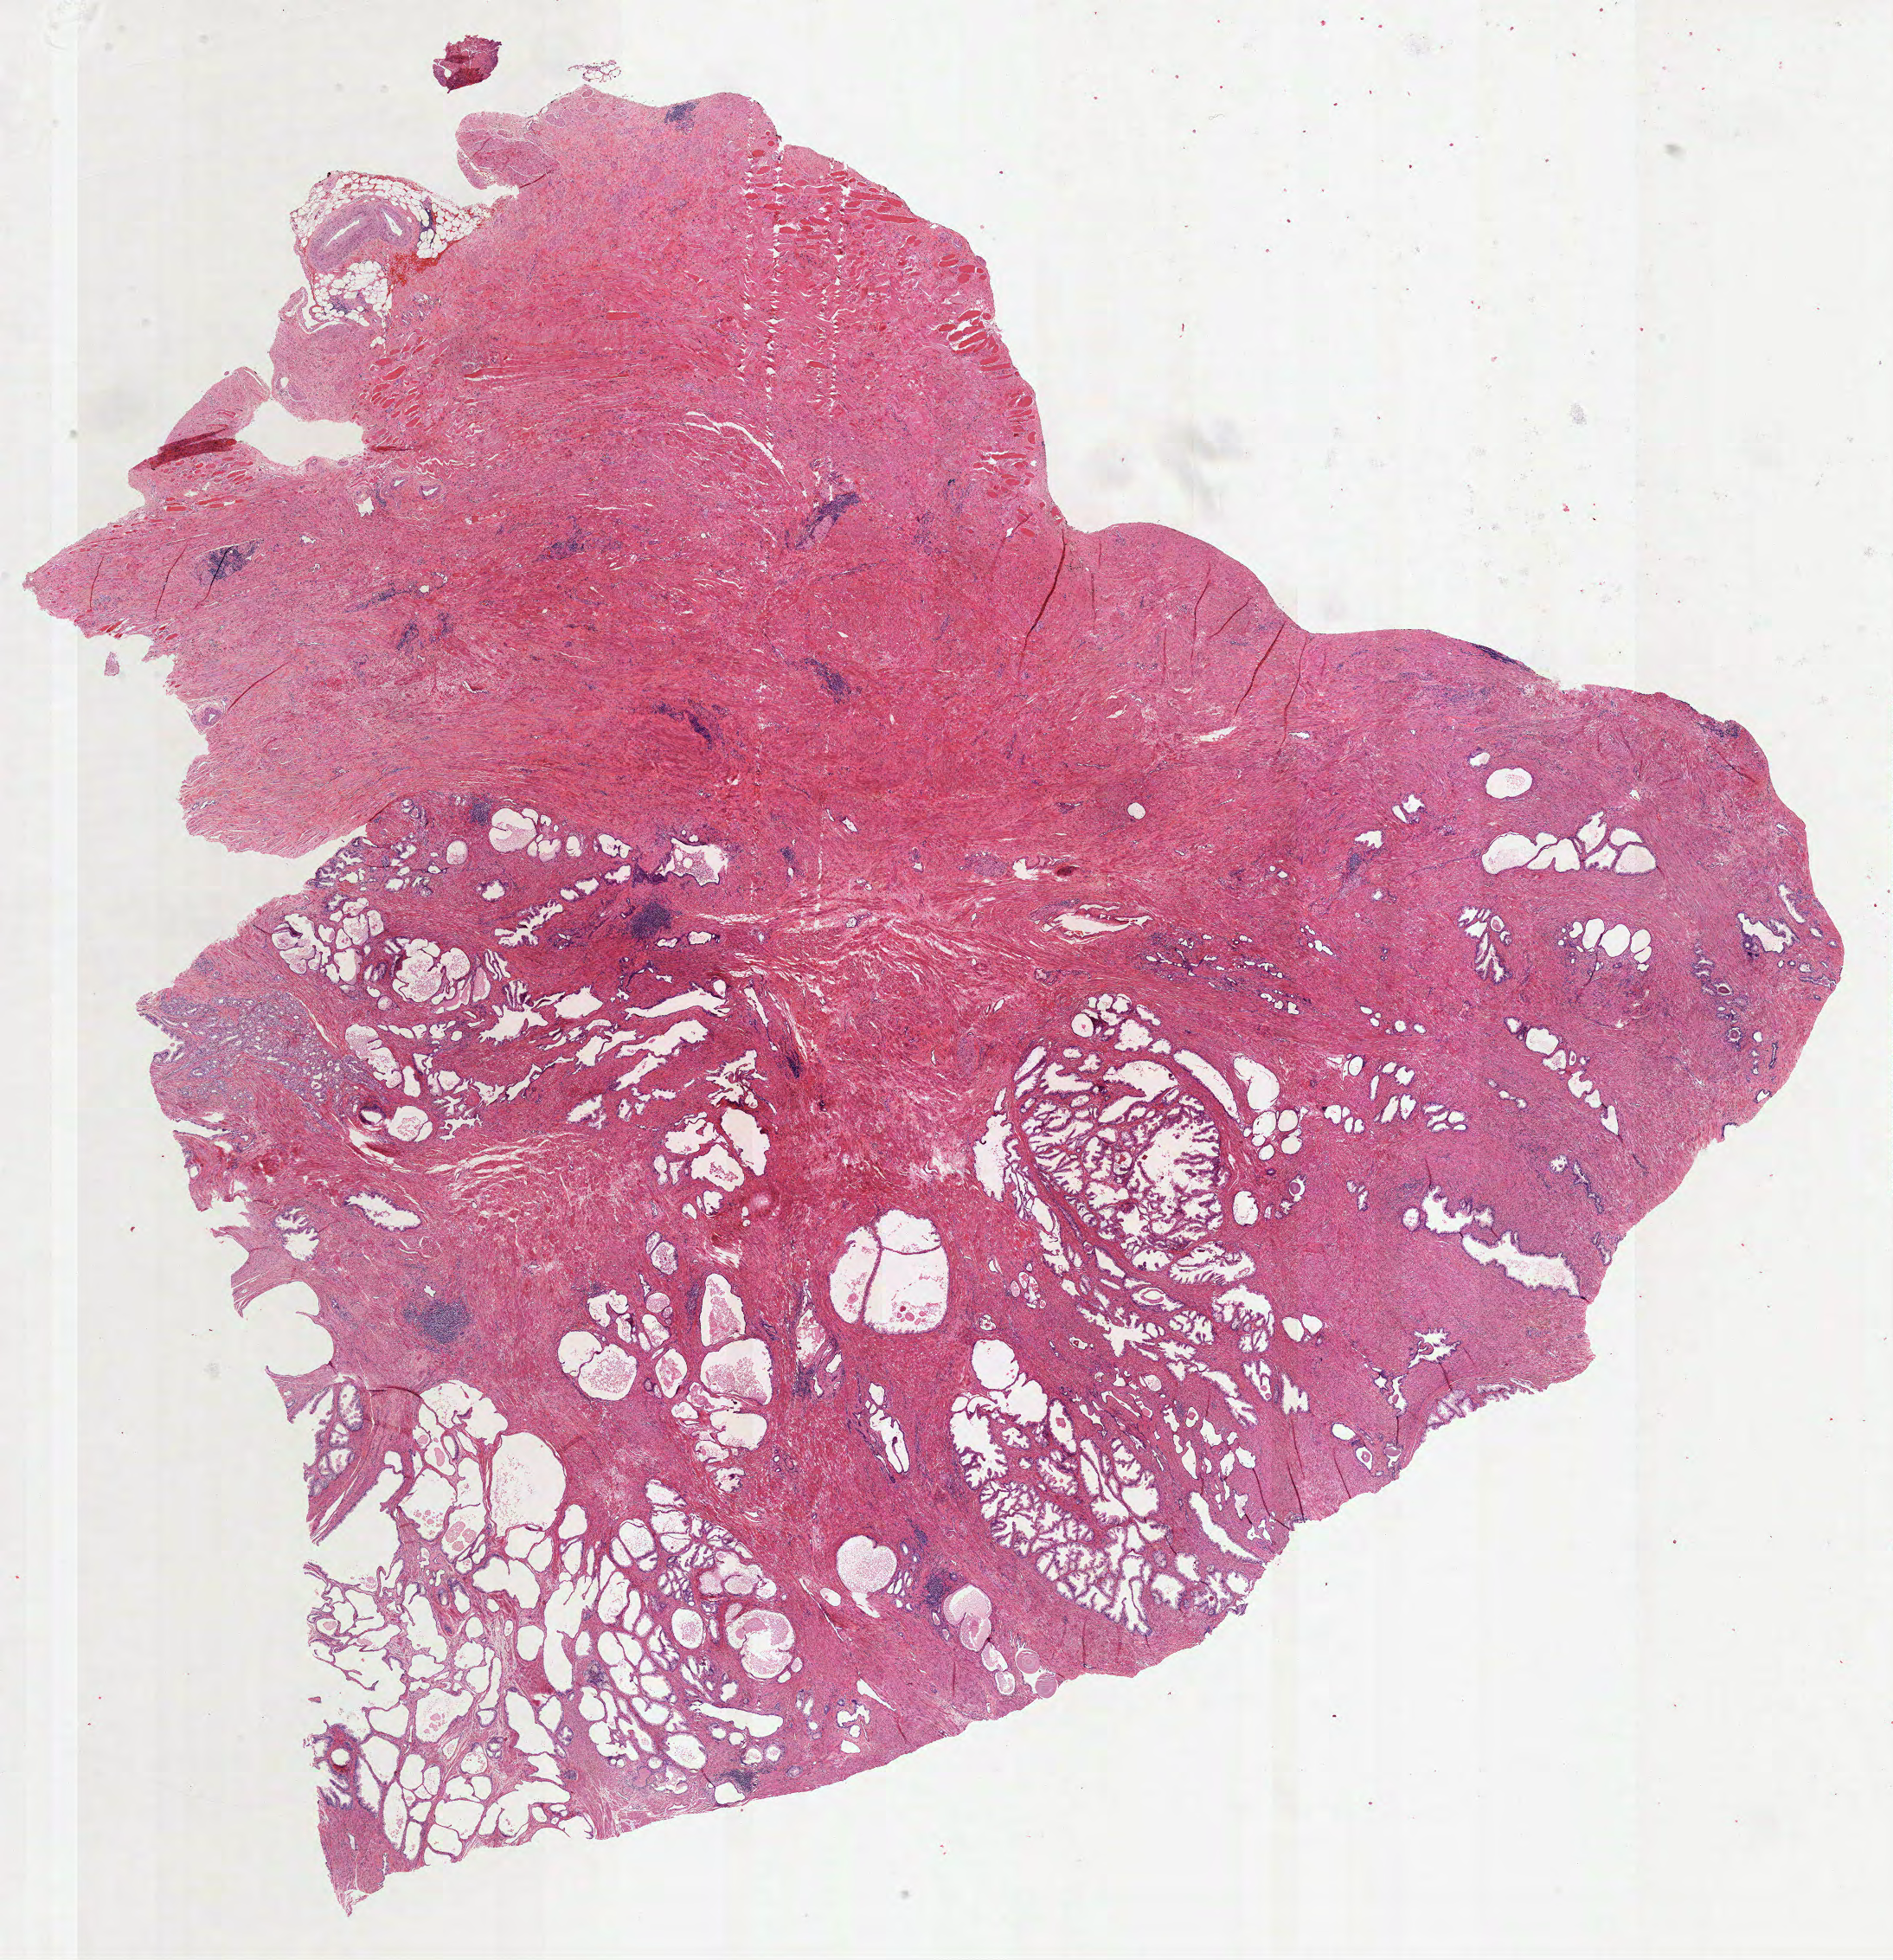
H&E whole-slide image — whole scanned area (about 17.6 x 18.3 mm, slide scanned at 40x) shown as a low-resolution overview, formalin-fixed paraffin-embedded (FFPE) diagnostic section, prostate, primary tumour sample. Male patient; age at initial diagnosis 65 years. Gleason score: 7 (4+3).
* pathologic diagnosis: Acinar cell carcinoma
* laterality: bilateral
* lymph nodes positive (case pathology): 0 of 21 examined